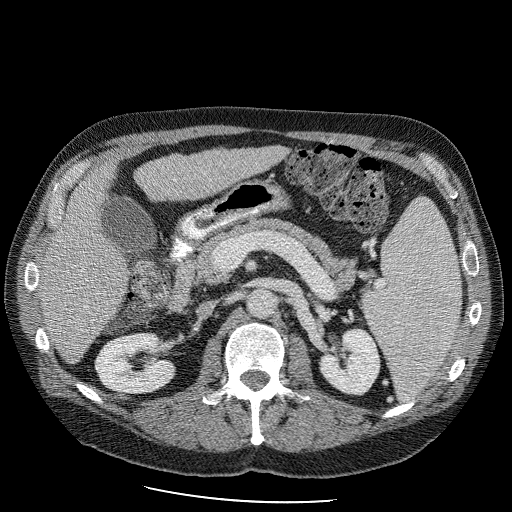
Contrast-enhanced abdominal CT (liver protocol), one axial slice. Position 40 of 98 along the scan axis. 120 kVp. Soft-tissue window (W 400 / L 40 HU). 2.5 mm slice thickness. 512 × 512 image matrix, field of view 400 × 400 mm. Case-level facts recorded for this patient, not image findings: diagnosis: hepatocellular carcinoma (patient treated with transarterial chemoembolisation; whether this scan precedes or follows treatment is not stated here); TNM stage (as recorded): Stage-II; Child-Pugh class: B; tumour differentiation: moderately differentiated; tumour nodularity: uninodular.
Outlined on this slice (semi-automatically segmented with operator editing):
- liver parenchyma outside the tumour (the mass and vessels are separate outlines, so this box may not span the whole liver): bounding box <36,144,293,364> (left, top, right, bottom; pixels)
- liver vessels: <54,221,56,223>